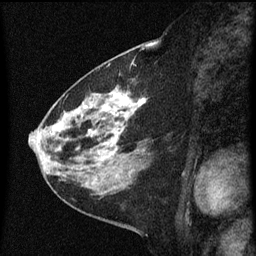
Breast MRI (dynamic contrast-enhanced), one sagittal slice; slice 26 of 60 in the series (ordered by position); dynamic contrast-enhanced series, image 2 of 3 at this slice position (ordered by acquisition); 1.5 T; TE 4.2 ms, TR 8 ms; 2 mm slice thickness; 256 × 256 image matrix, field of view 180 × 180 mm. Patient: female, 60 years.
Outlined on this slice (semi-automatic segmentation, software-assisted and operator-edited):
- analysis volume of interest (the breast-tissue region the enhancement analysis was run in; not a lesion): bounding box <48,82,152,183> (left, top, right, bottom; pixels)
- tumour enhancement mask (voxels above the 70 % enhancement threshold inside the analysis volume of interest): <53,92,145,159>